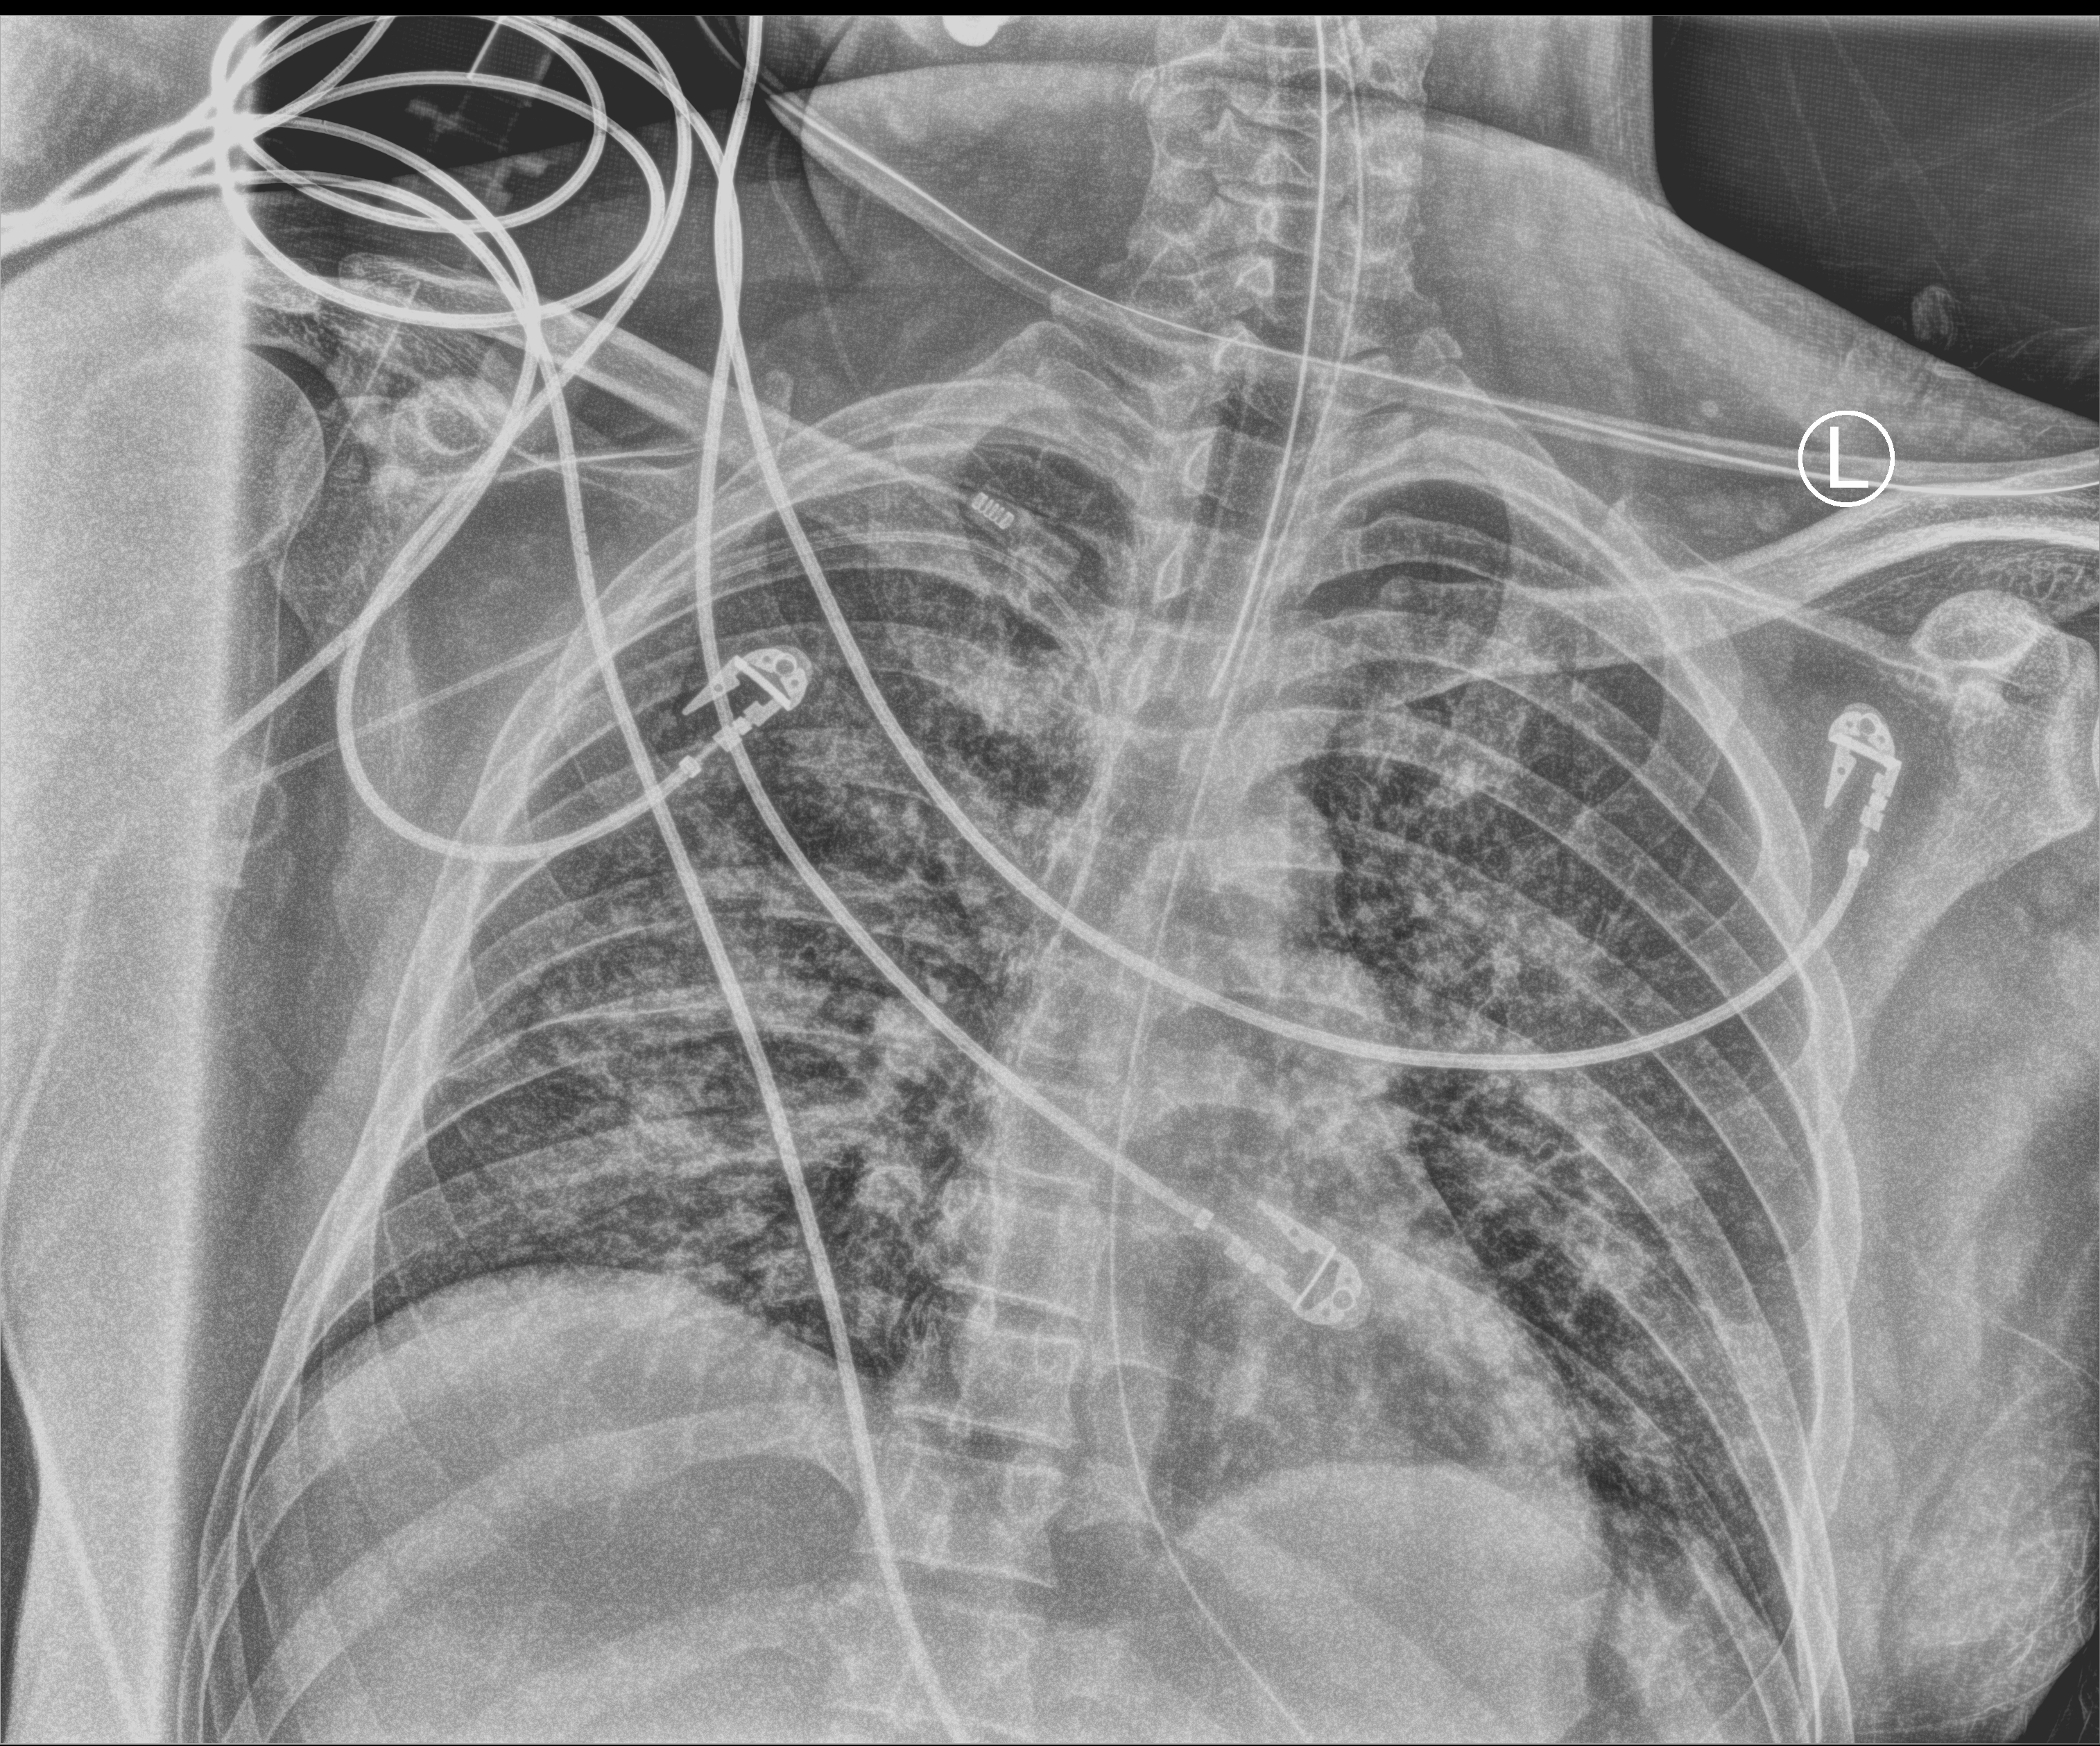
Portable chest radiograph; anteroposterior (AP) projection. Adult patient hospitalised with COVID-19, age 18–59 years.
Hospital-stay facts (about this admission, not read from this image; timing relative to this image not recorded):
- mechanically ventilated during this hospital stay: yes
- admitted to intensive care during this hospital stay: yes